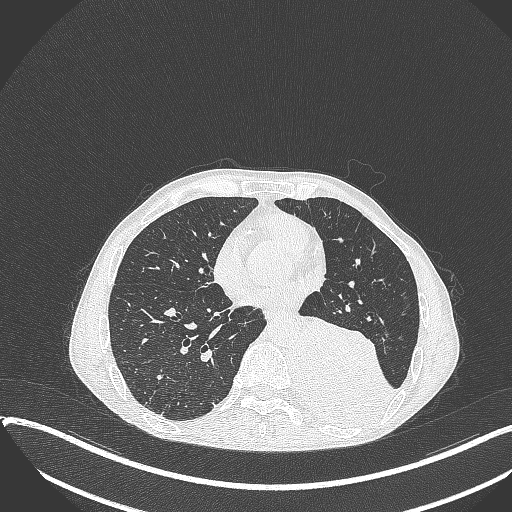
Chest CT, one axial slice. Slice 146 of 401 in the series (ordered by position). Reconstruction kernel B70f. Lung window (W 1500 / L -600 HU). 1 mm slice thickness. 512 × 512 image matrix, field of view 400 × 400 mm. Male patient, age 57 years. From the clinical record (not read from this slice): clinical TNM (as recorded): T4 N0 M0.
Structures marked on this image (bounding box drawn by a radiologist):
- lung tumour (recorded histology: squamous cell carcinoma): box from (x=291, y=311) to (x=401, y=423) px